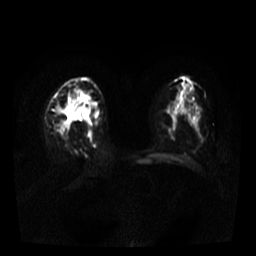
Breast MRI, one axial slice; diffusion-weighted series; image 2 of 4 stored at this slice position (different b-values; order by instance number); 3 T; 256 × 256 image matrix, field of view 320 × 320 mm. Female patient.
Structures marked on this image (manually delineated by an expert):
- tumour on diffusion-weighted imaging: box from (x=58, y=104) to (x=74, y=133) px